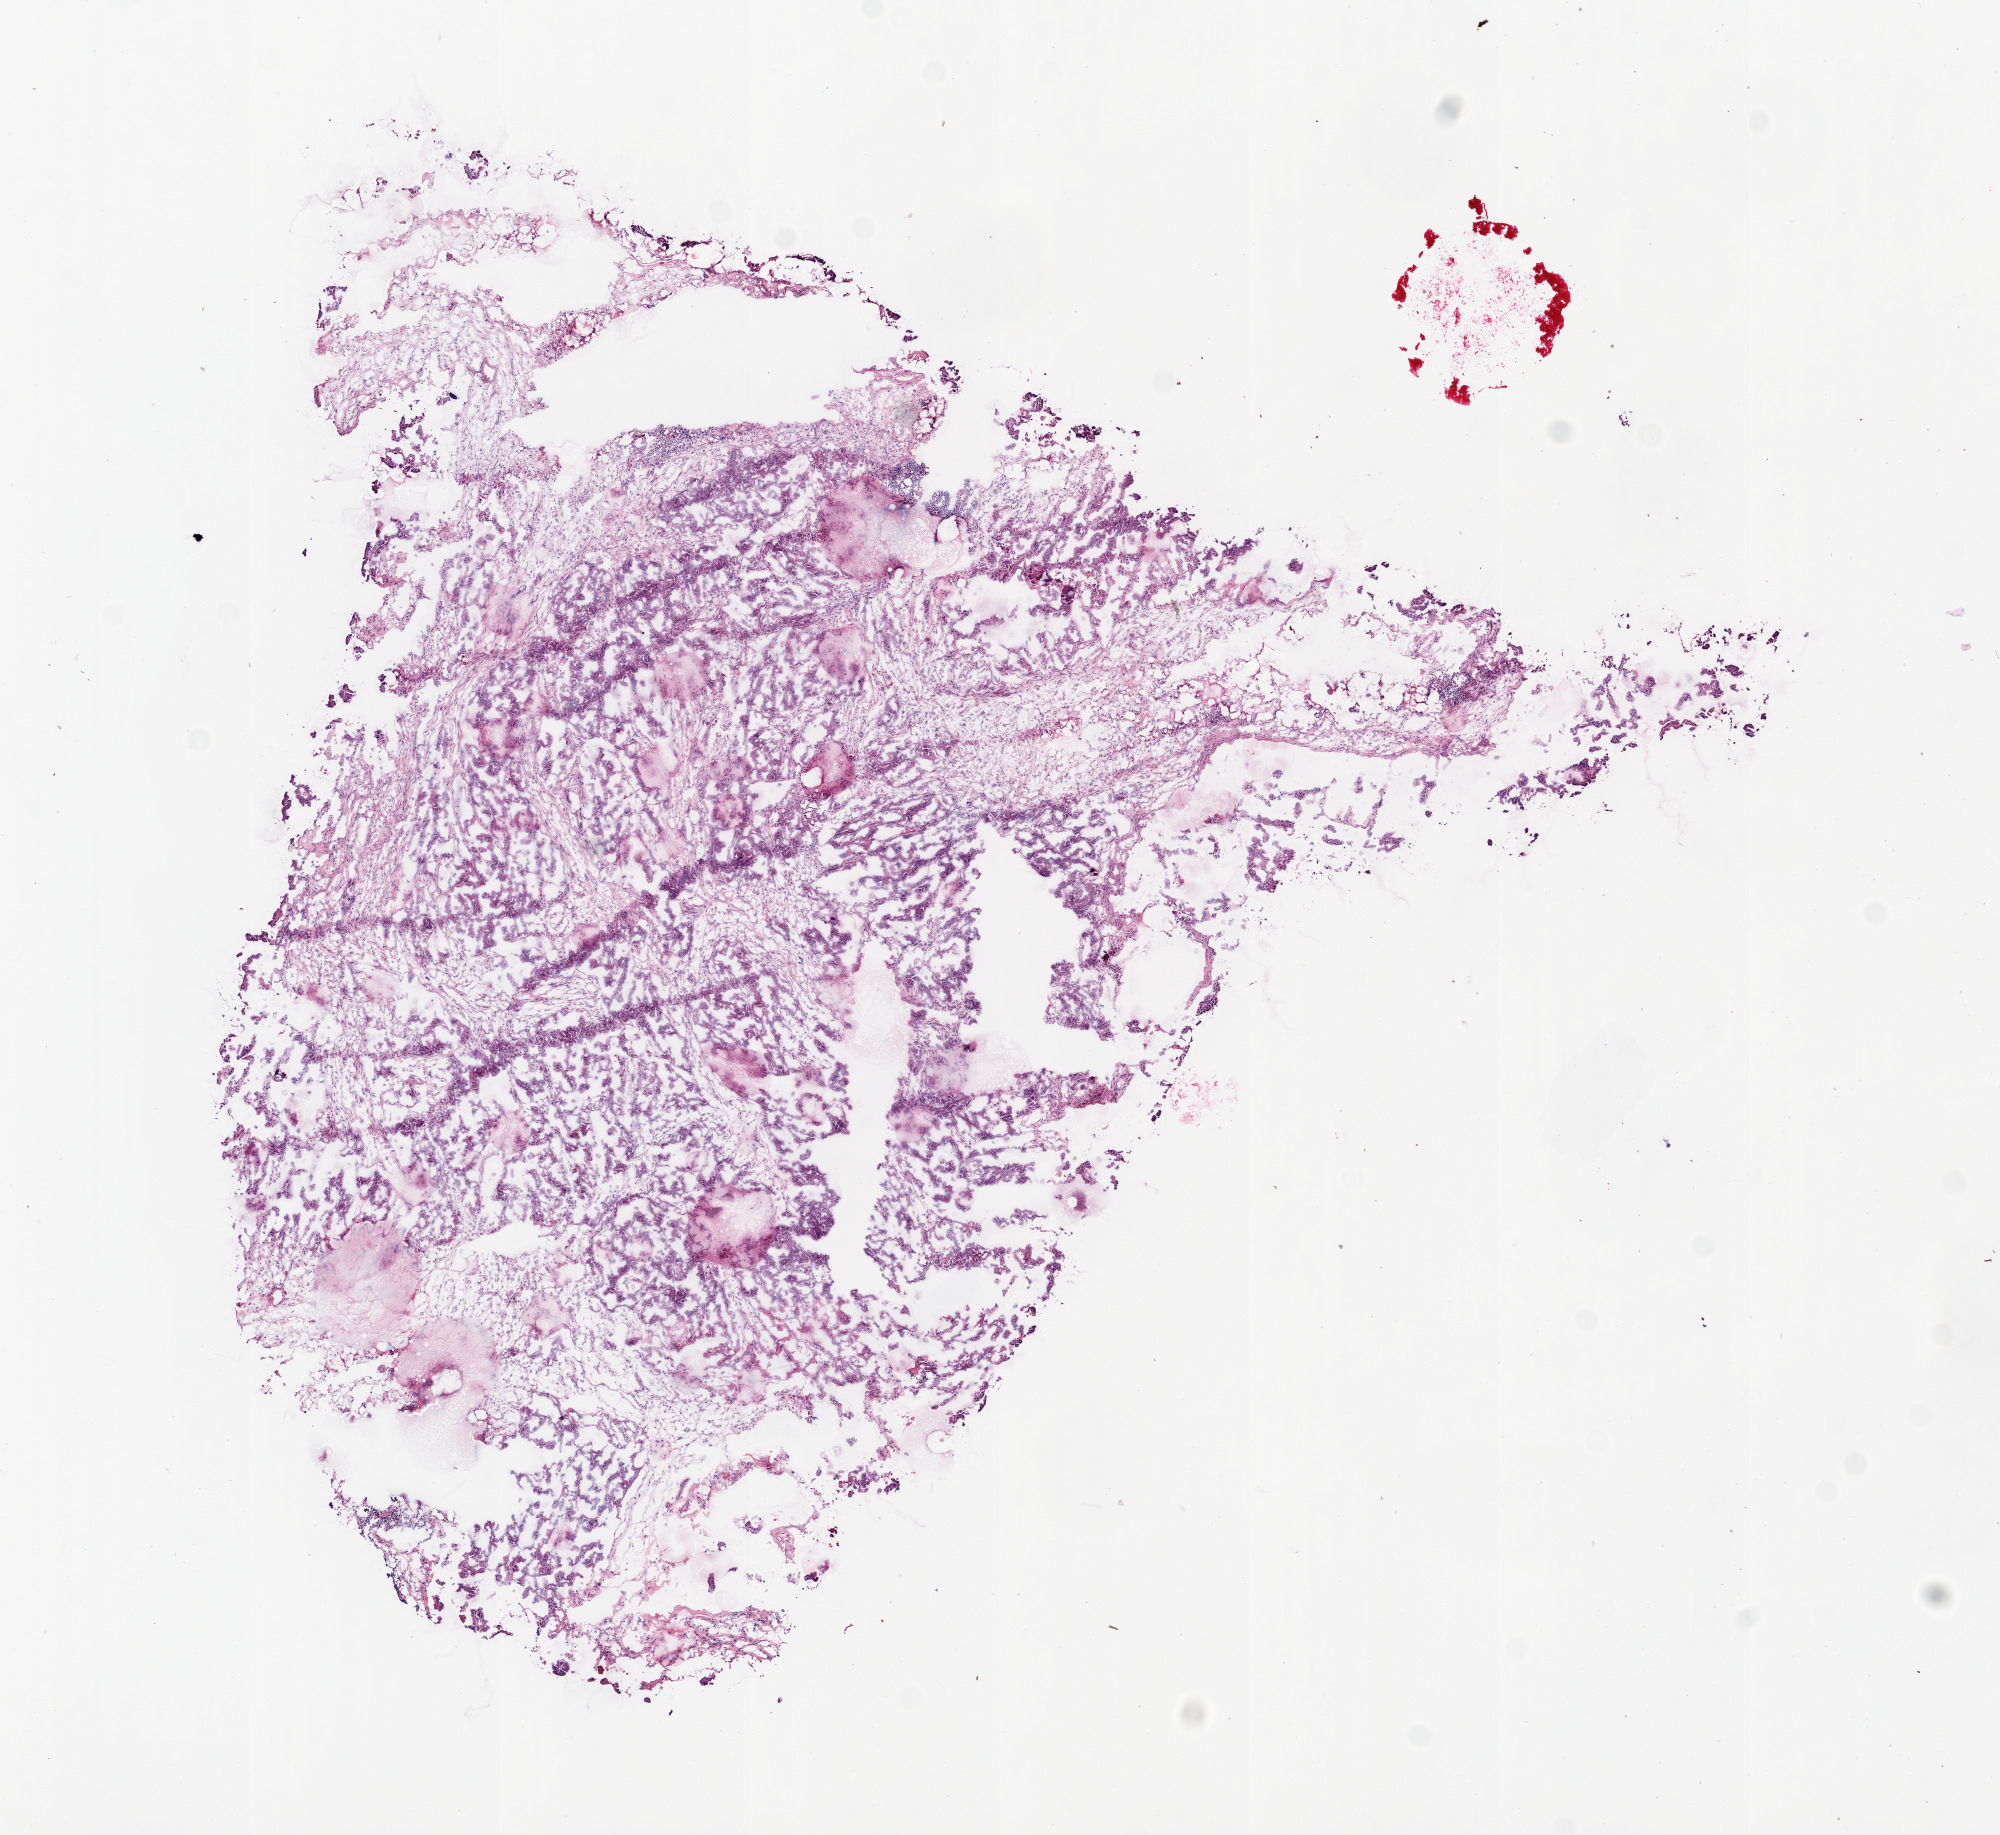
H&E-stained whole-slide image, a low-resolution overview of the entire scanned area, about 8.0 x 7.4 mm (from a 20x scan); frozen section from the bottom of the tissue portion; ovary, primary tumour sample. Patient: female, age at initial diagnosis 58 years. Histologic grade: G2 (moderately differentiated). Composition of this section per pathologist review: tumour cells 70%, tumour nuclei 80%, normal cells 0%, stromal cells 20%, necrosis 10%.
Laterality: right. Histologic diagnosis: Serous cystadenocarcinoma, NOS. FIGO stage: IIIC.